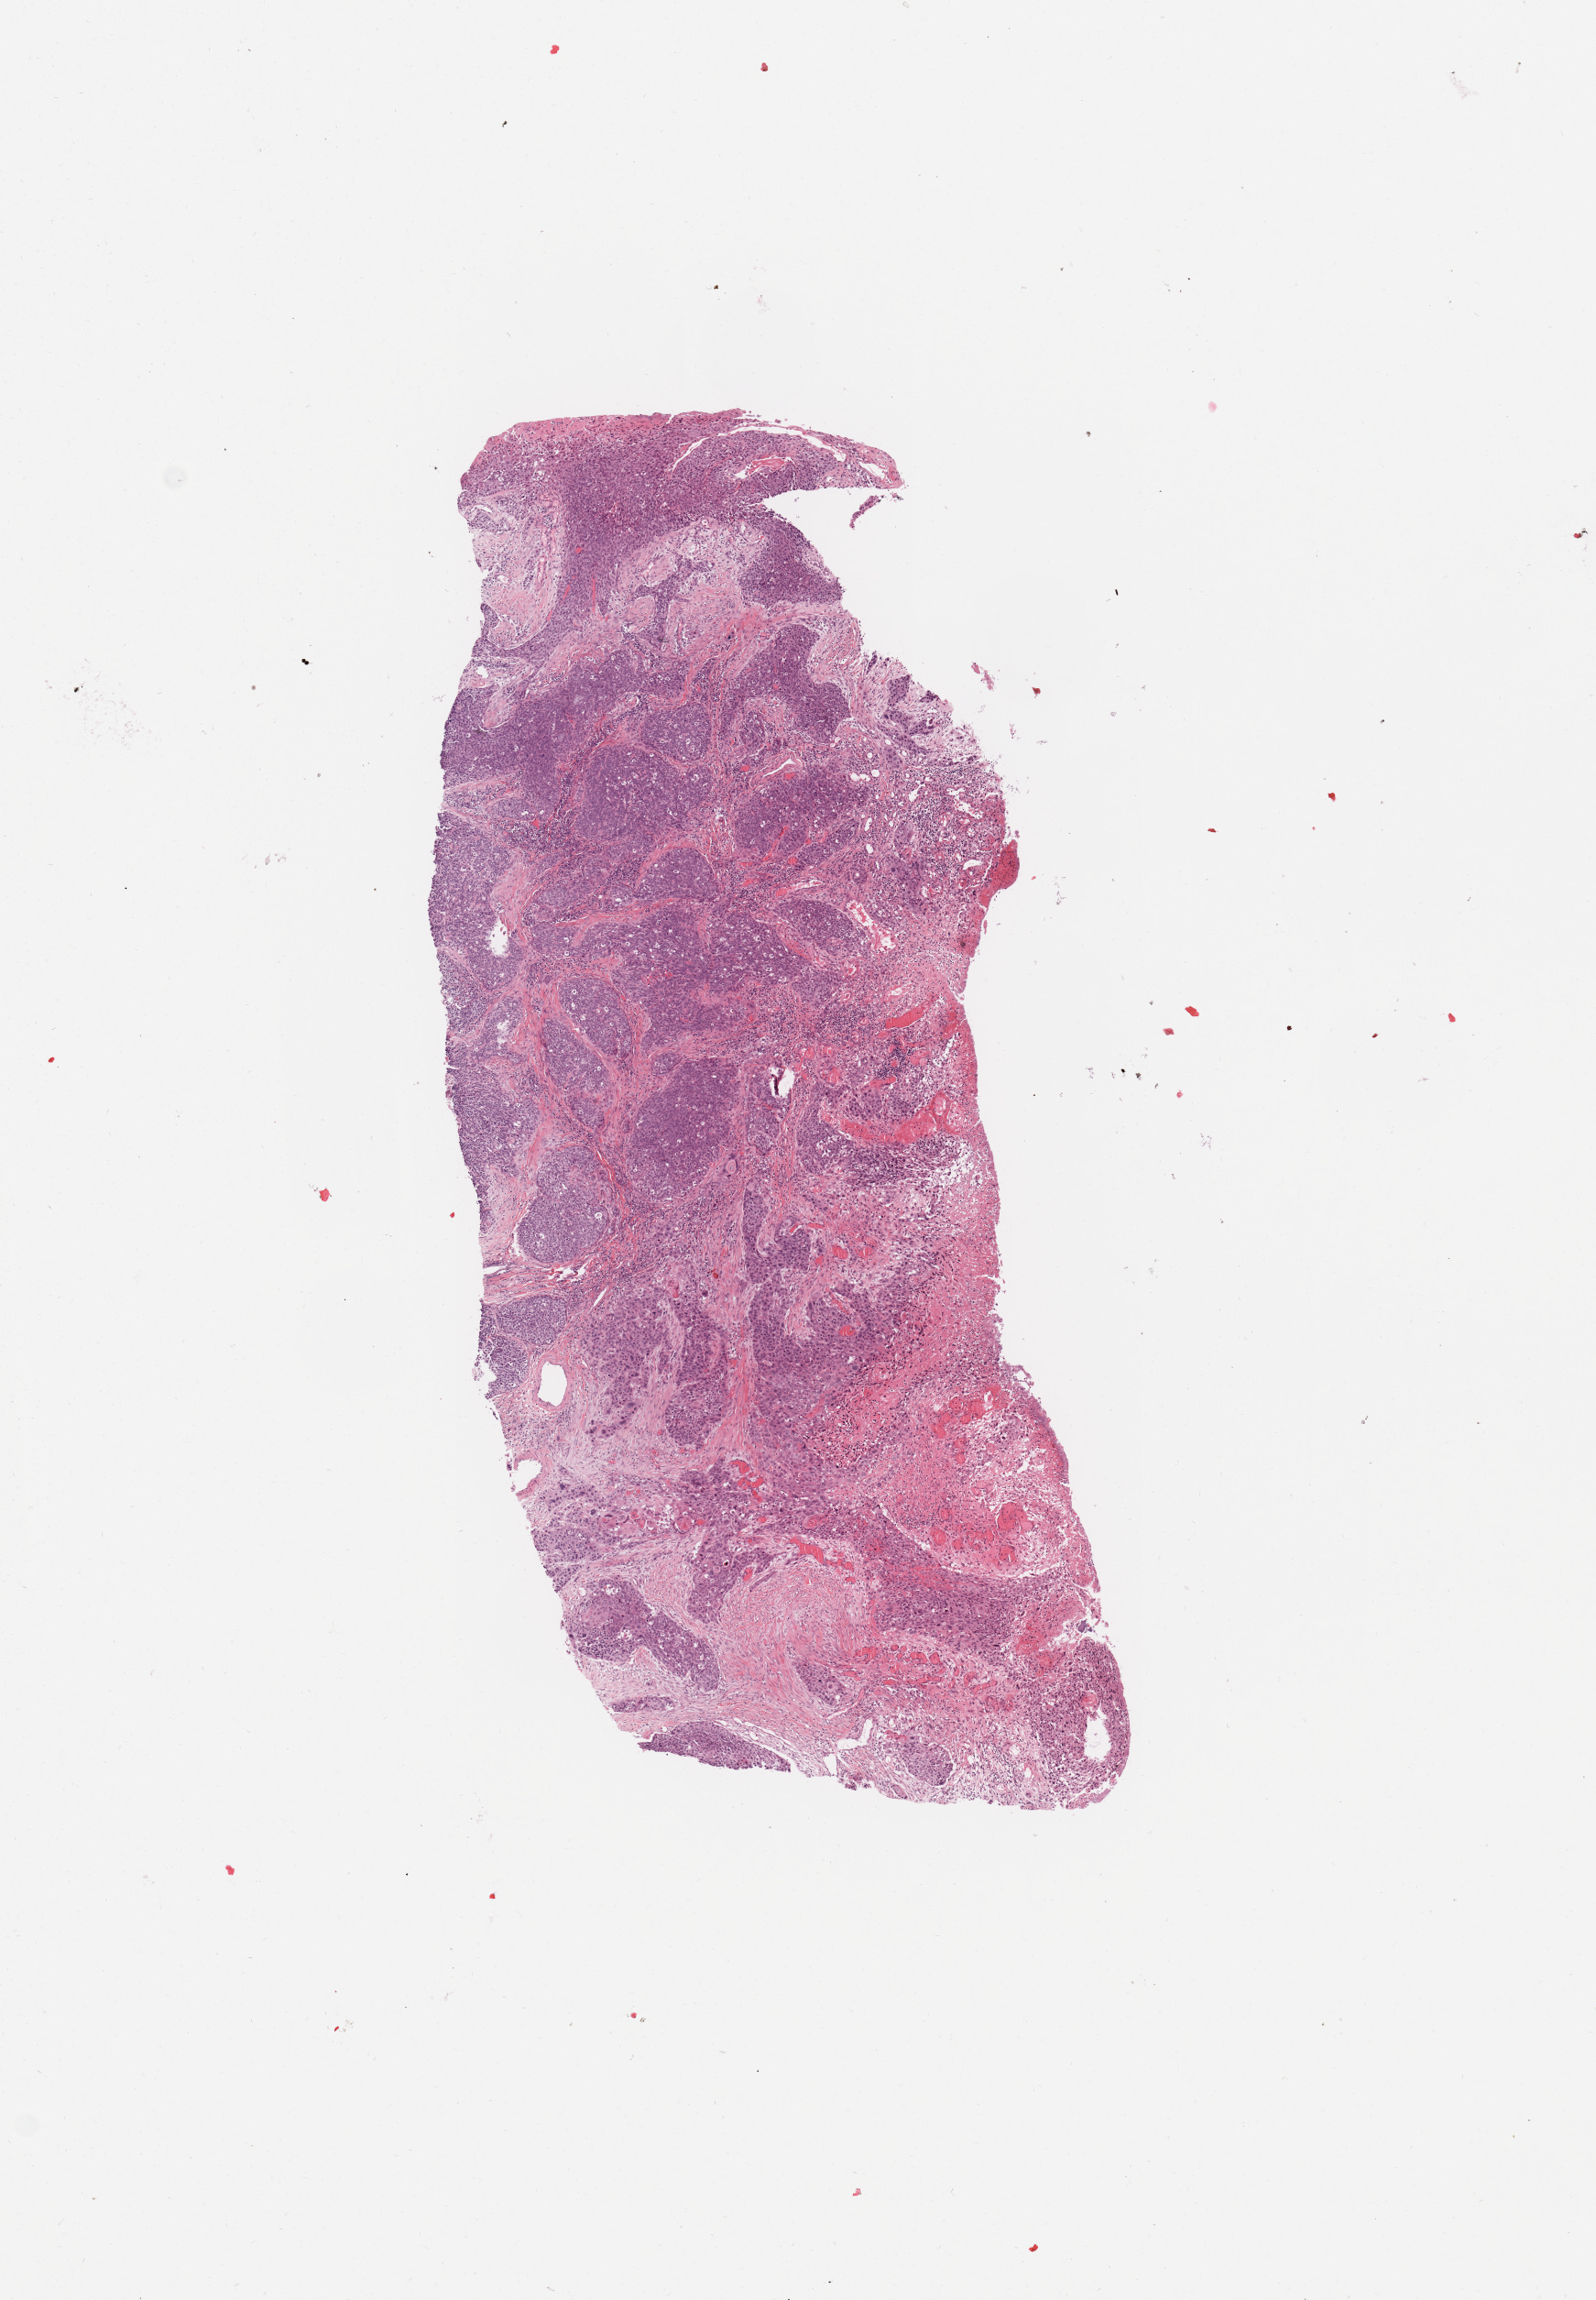
Digitized H&E-stained tissue section (whole slide), low-resolution overview of the scanned area, about 6.9 x 9.9 mm; tumour tissue sample, sampled site: larynx. Patient: male, age 65 years. Composition of this section per pathologist review: tumour nuclei 80%, necrosis 5%.
Histologic diagnosis: Squamous cell carcinoma, NOS.